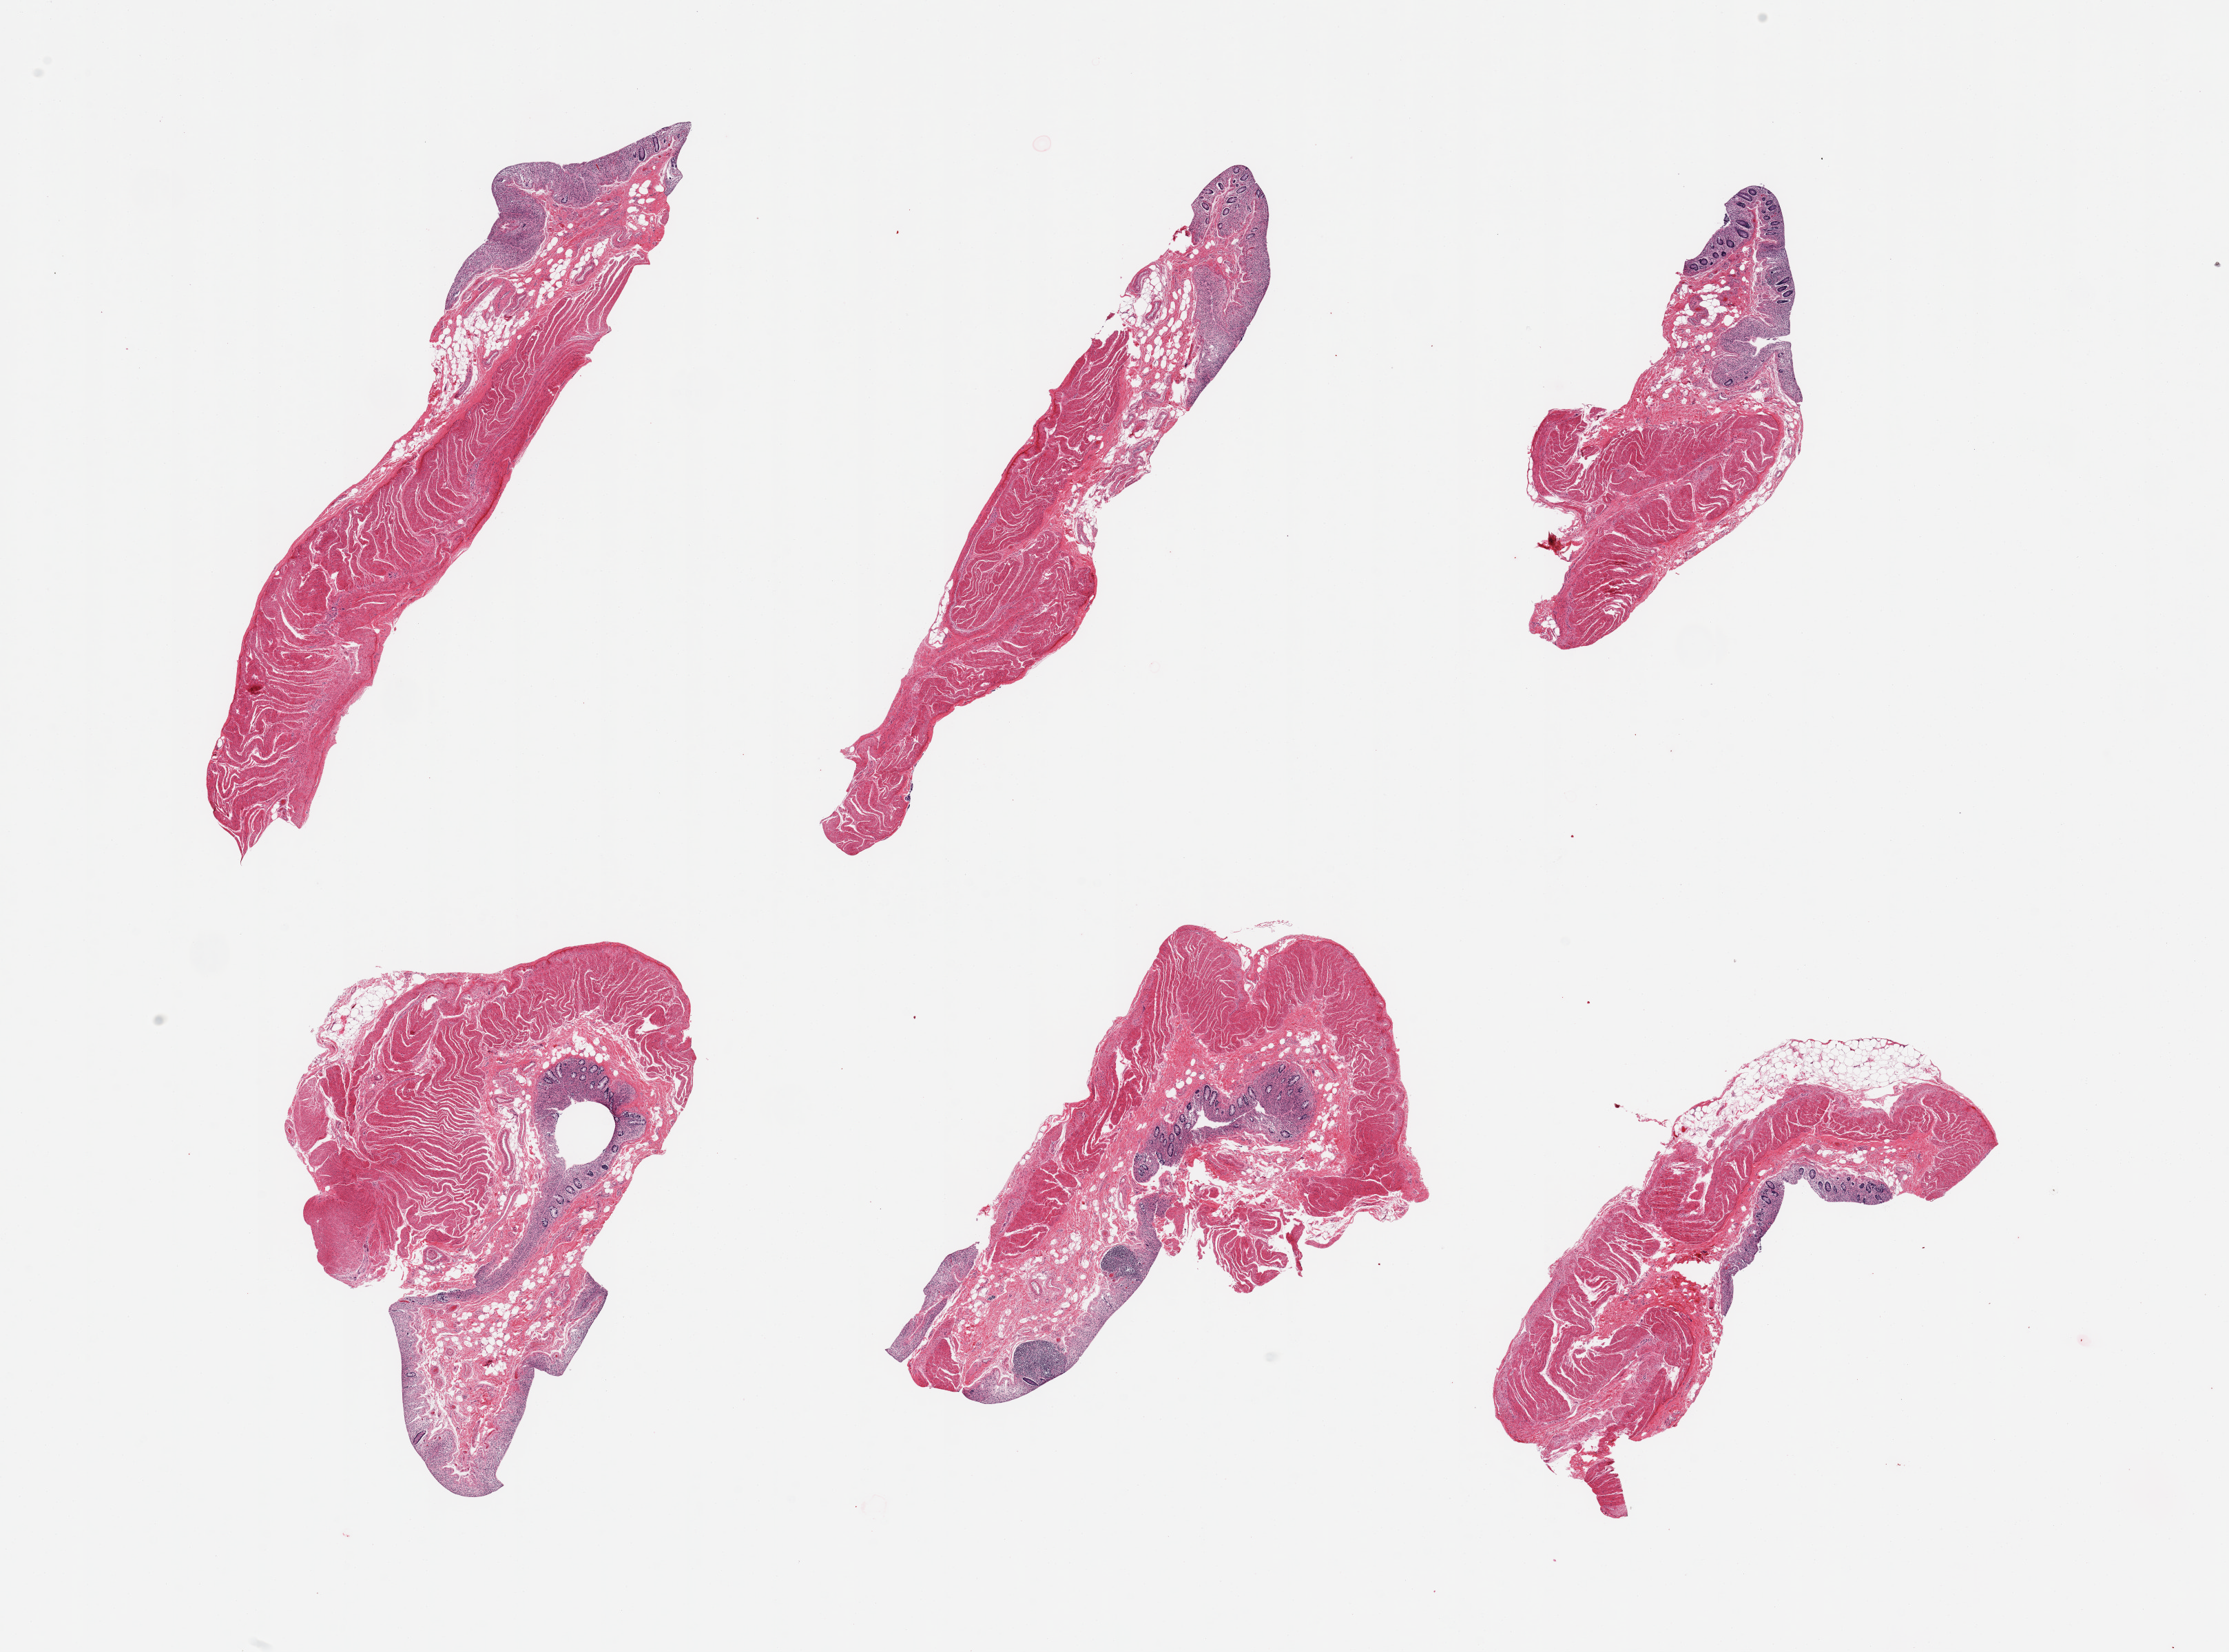
Haematoxylin and eosin whole-slide image, shown as a low-resolution overview of the whole scanned area (about 25.6 x 19.0 mm); PAXgene-fixed paraffin-embedded (PFPE) section; section of transverse colon (target tissue); donor tissue sample. Donor: male.
• review note (as recorded): 6 pieces; largely autolyzed mucosa, intact muscularis